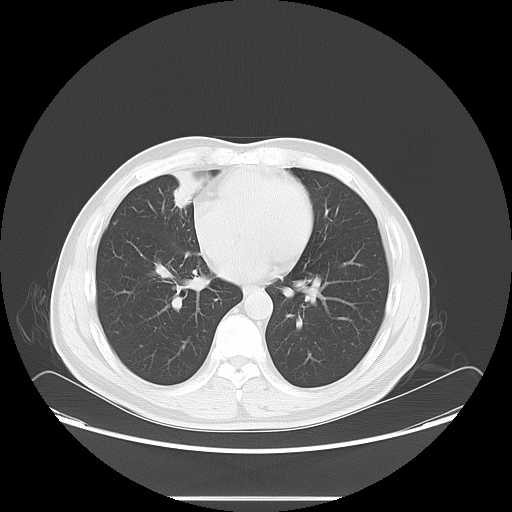
Chest CT, one axial slice. Slice 34 of 73 in the series (ordered by position). Reconstruction kernel LUNG. Lung window (W 1500 / L -600 HU). 512 × 512 image matrix. Patient: male, 47 years. Case-level facts recorded for this patient, not image findings: clinical TNM (as recorded): T1c N3 M0.
Structures marked on this image (bounding box drawn by a radiologist):
- lung tumour (recorded histology: adenocarcinoma): bounding box [x1, y1, x2, y2] px = [172, 175, 205, 212]